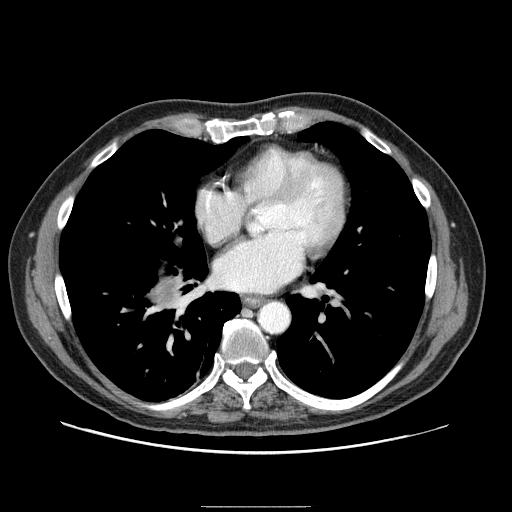
Contrast-enhanced abdominal CT (liver protocol), one axial slice. Position 91 of 99 along the scan axis. Reconstruction kernel STANDARD. 100 kVp. One of 2 acquisitions stored at this slice position. Soft-tissue window (W 400 / L 40 HU). 2.5 mm slice thickness. 512 × 512 image matrix, field of view 400 × 400 mm. Case-level facts recorded for this patient, not image findings: diagnosis: hepatocellular carcinoma (patient treated with transarterial chemoembolisation; whether this scan precedes or follows treatment is not stated here); TNM stage (as recorded): Stage-II; Child-Pugh class: A; tumour differentiation: well differentiated.
Structures marked on this image (semi-automatically segmented with operator editing):
- liver parenchyma outside the tumour (the mass and vessels are separate outlines, so this box may not span the whole liver): bounding box <164,294,170,300> (left, top, right, bottom; pixels)